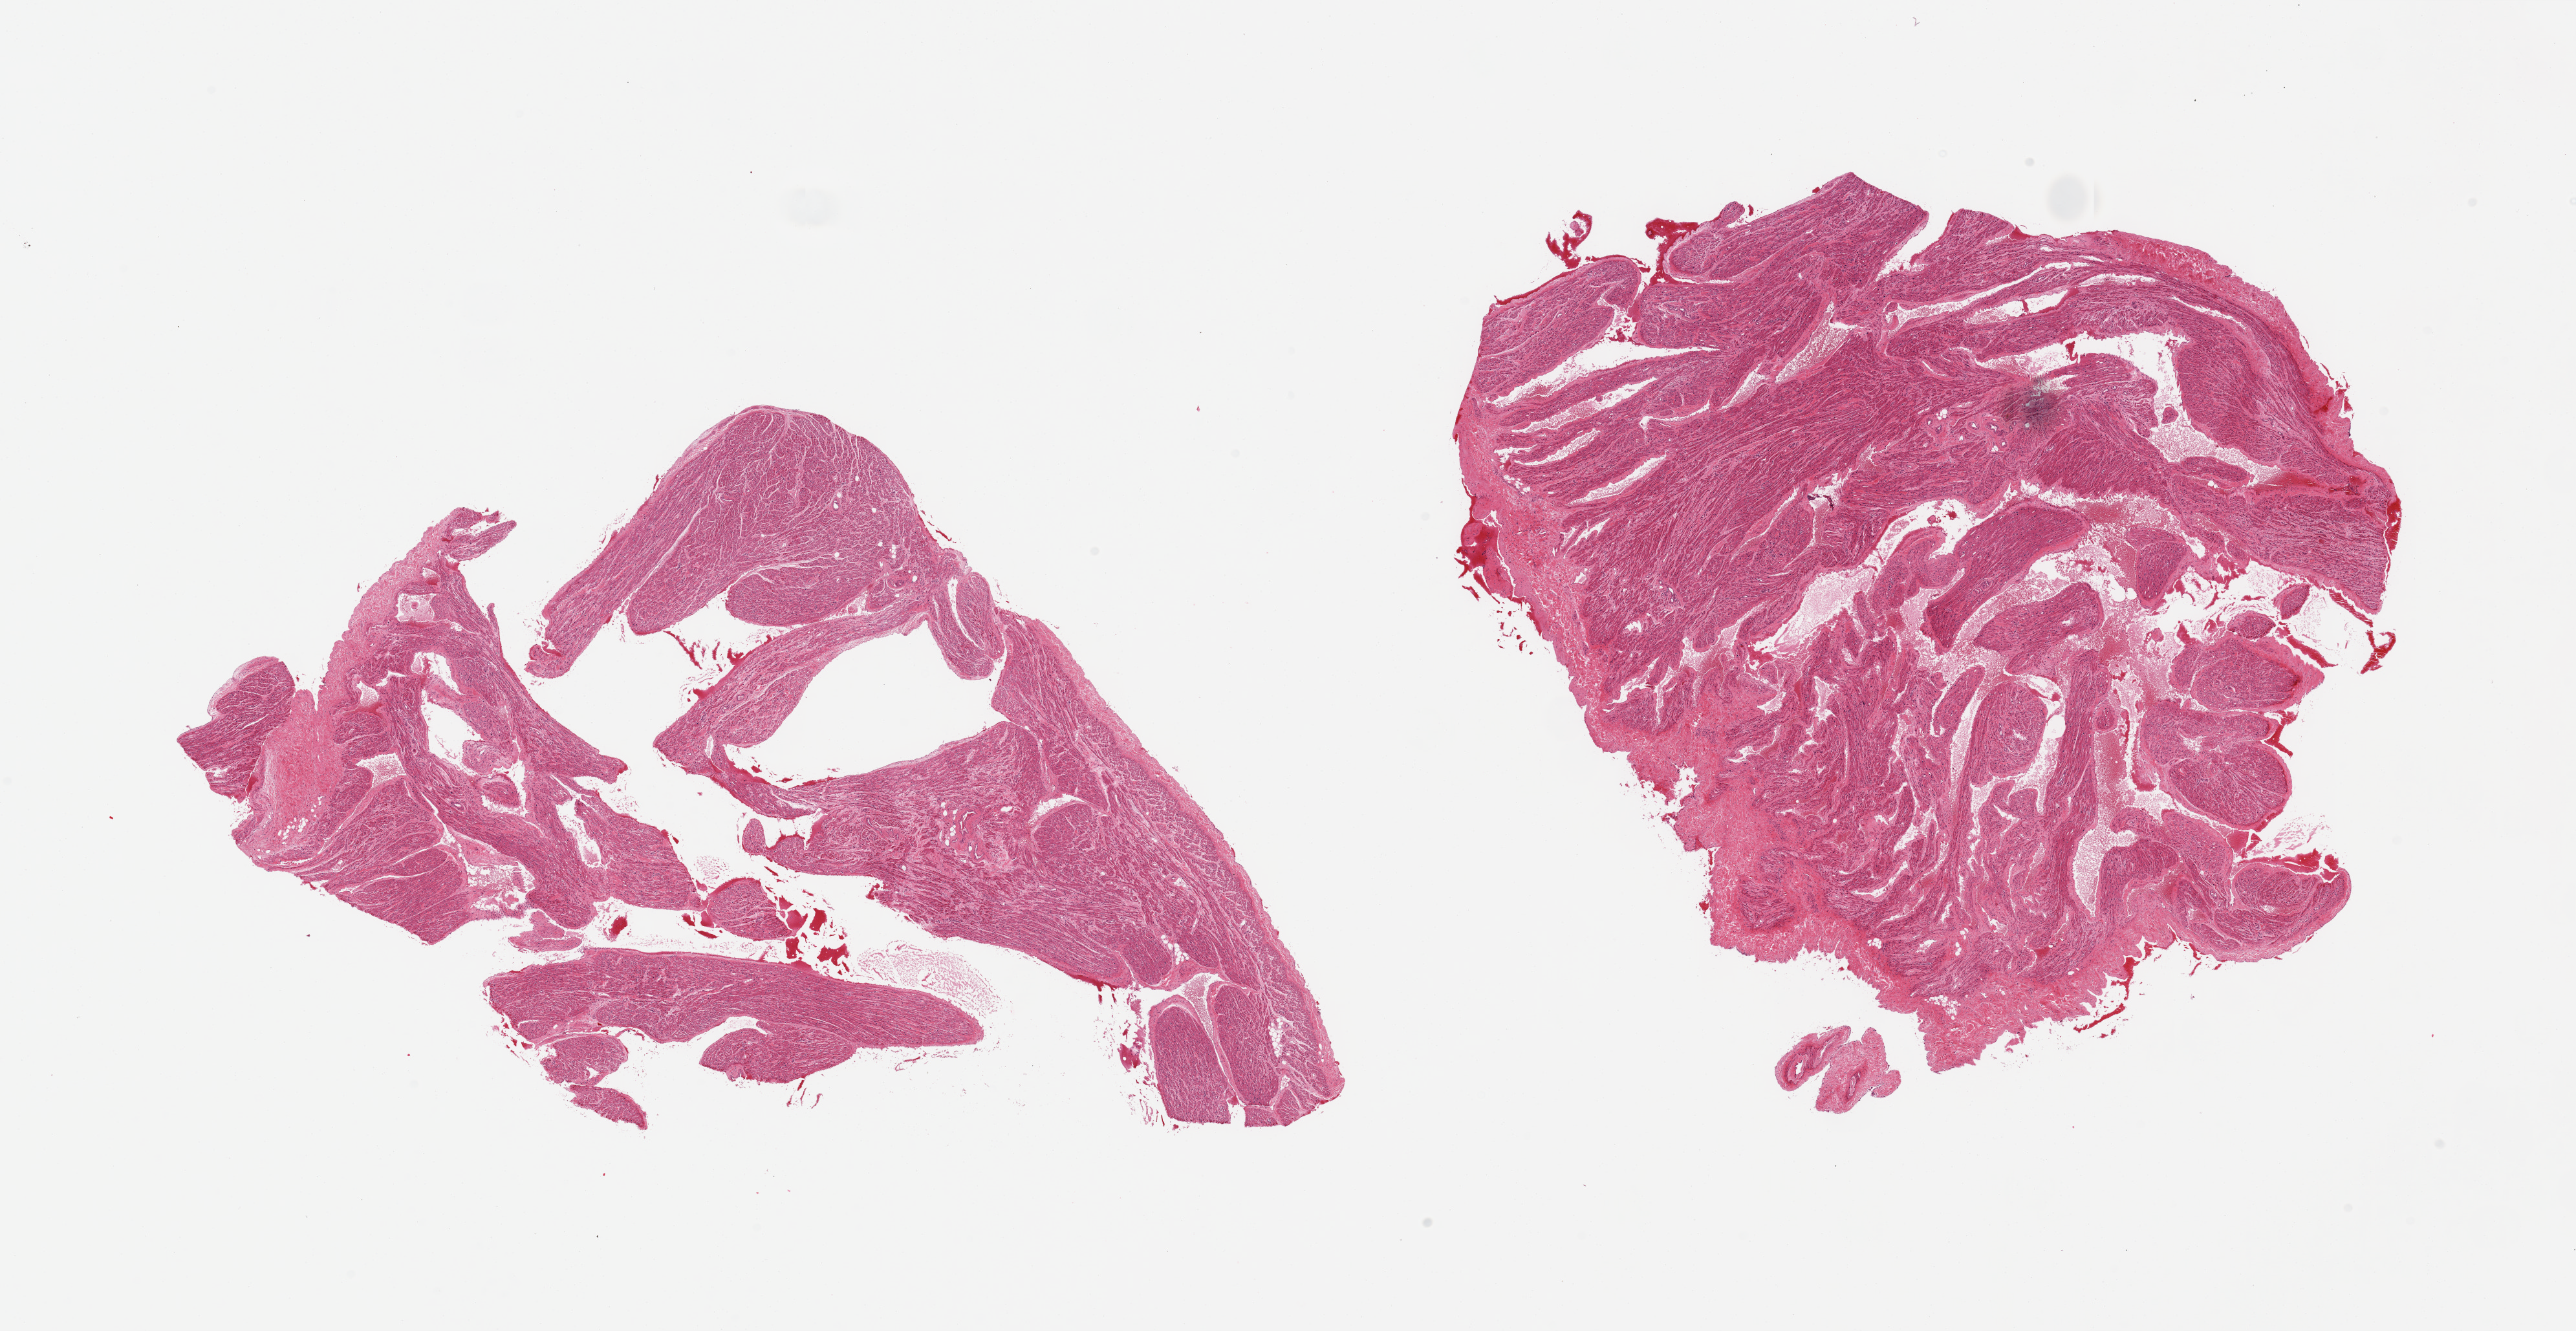
Whole-slide image, haematoxylin and eosin stain, brightfield — shown as a low-resolution overview of the whole scanned area (about 31.5 x 16.3 mm); PAXgene-fixed, paraffin-embedded tissue; target tissue: auricular appendage; donor tissue sample. Male donor.
- pathologist's review note for this sample: 2 pieces; low fat & fibrous content